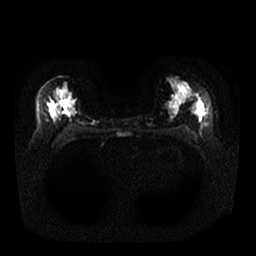
Breast MRI, one axial slice. Position 14 of 25 along the scan axis. Diffusion-weighted series; image 2 of 4 stored at this slice position (different b-values; order by instance number). 1.5 T. 256 × 256 image matrix, field of view 340 × 340 mm. Female patient.
Annotated regions visible in this slice (expert manual segmentation):
- tumour on diffusion-weighted imaging: bounding box <51,108,57,118> (left, top, right, bottom; pixels)